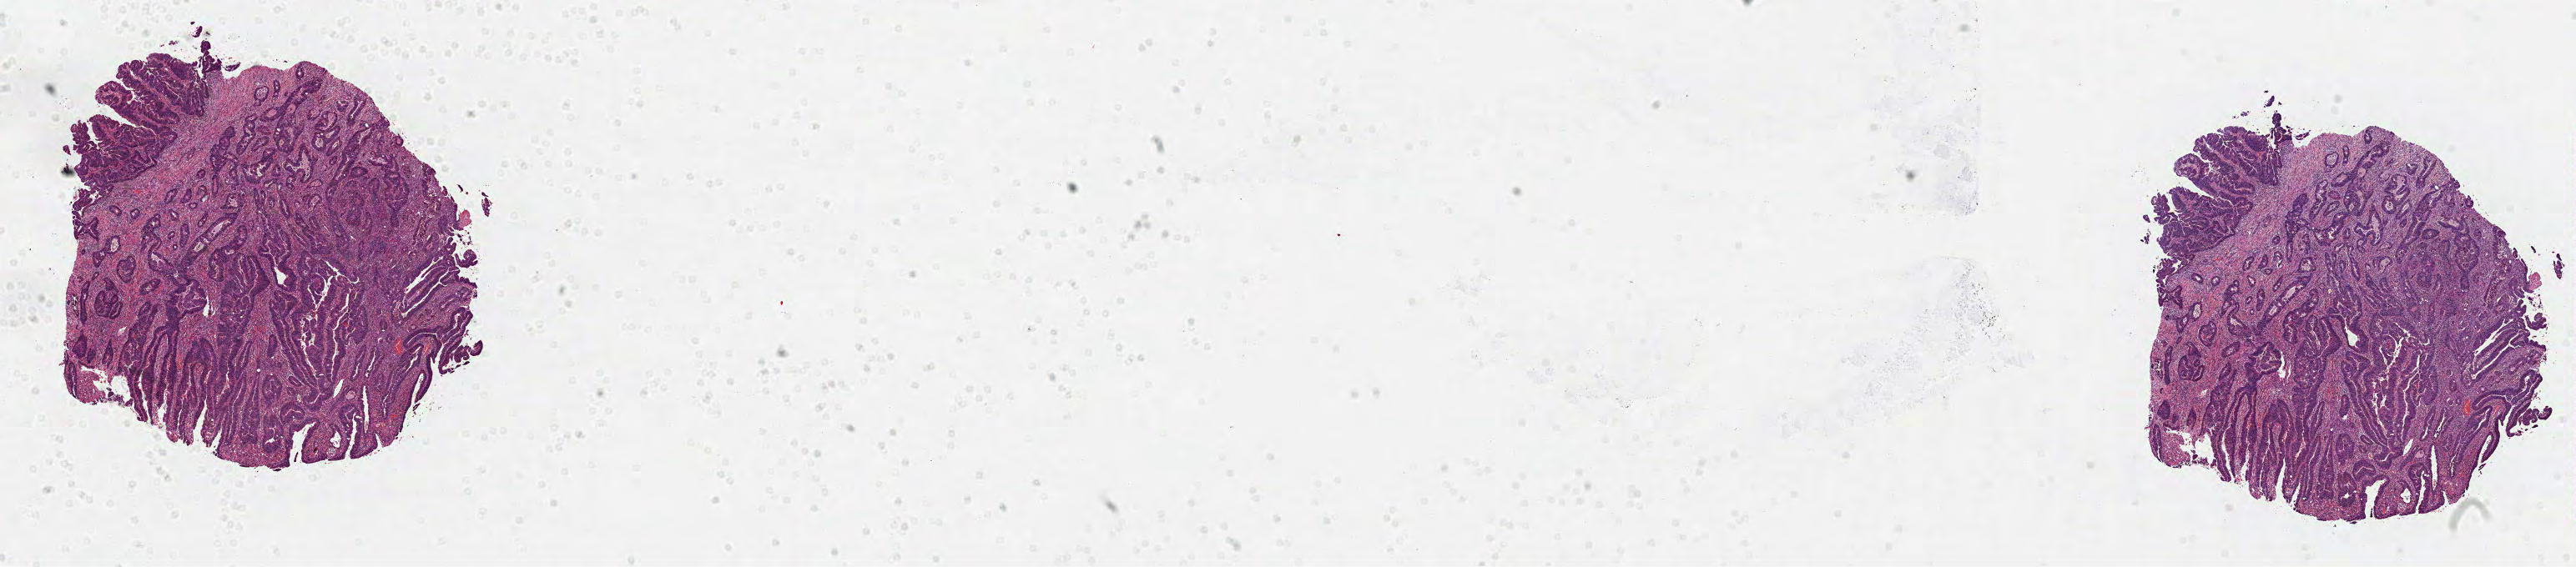
H&E-stained whole-slide image, a low-resolution overview of the entire scanned area, about 24.9 x 5.5 mm; formalin-fixed paraffin-embedded (FFPE) diagnostic section; primary tumour sample from the colon. Female patient; age at initial diagnosis 40 years.
AJCC pathologic stage: IIIB (7th edition). Lymph nodes positive (case pathology): 1 of 48 examined. Pathologic diagnosis: Adenocarcinoma, NOS (sigmoid colon).